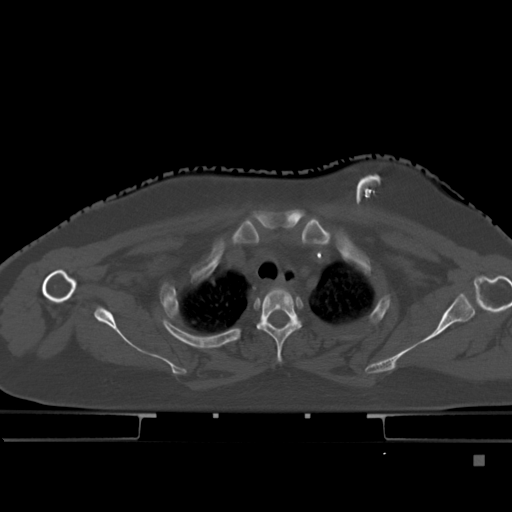
CT including the spine, one axial slice. Position 358 of 495 along the scan axis. Bone window (W 1800 / L 400 HU). 1.5 mm slice thickness. 512 × 512 image matrix, field of view 404 × 404 mm. Patient: female, 33 years. From the clinical record (not read from this slice): primary cancer: breast; vertebrae with lytic lesions (as recorded): T1.
Structures marked on this image (semi-automatically segmented with operator editing):
- T1 vertebra: bounding box <269,288,277,292> (left, top, right, bottom; pixels)
- T2 vertebra: <257,288,301,364>